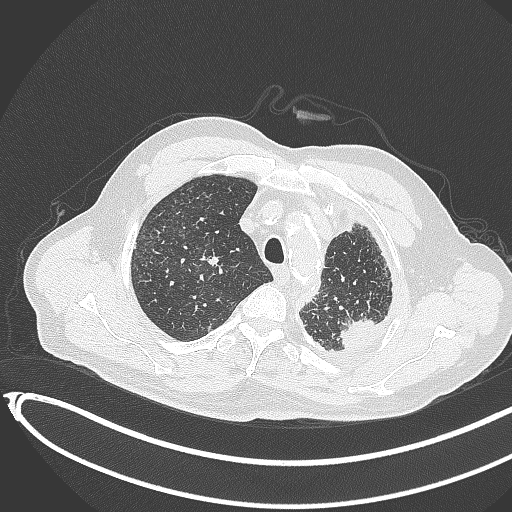
Chest CT, one axial slice. Lung window (W 1500 / L -600 HU). 1 mm slice thickness. 512 × 512 image matrix, field of view 400 × 400 mm. Patient: male, 78 years. Case-level facts recorded for this patient, not image findings: clinical TNM (as recorded): T1c N0 M1.
Annotated regions visible in this slice (bounding box drawn by a radiologist):
- lung tumour (recorded histology: adenocarcinoma): bounding box (x1, y1, x2, y2) in pixels: (337, 311, 380, 354)